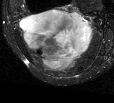
MRI of an extremity soft-tissue mass, one axial slice. Position 28 of 44 along the scan axis. T2-weighted fat-saturated. MR volume resampled by the dataset authors to the PET/CT grid (not the native acquisition matrix). 114 × 103 image matrix, field of view 111 × 101 mm. Female patient. Case-level facts recorded for this patient, not image findings: histological type: liposarcoma; site of the primary tumour: right thigh.
Annotated regions visible in this slice (expert contour drawn on MRI and transferred to this co-registered scan by the dataset authors):
- gross tumour volume (mass): box from (x=20, y=9) to (x=94, y=72) px